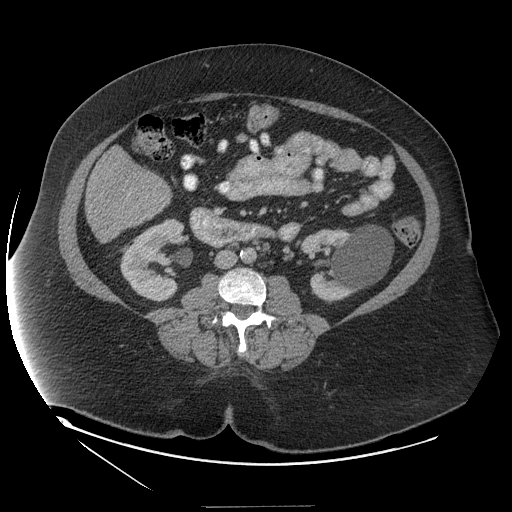
Contrast-enhanced abdominal CT (liver protocol), one axial slice; slice 34 of 127 in the series (ordered by position); reconstruction kernel STANDARD; 140 kVp; soft-tissue window (W 400 / L 40 HU); 2.5 mm slice thickness; 512 × 512 image matrix, field of view 480 × 480 mm. Case-level facts recorded for this patient, not image findings: diagnosis: hepatocellular carcinoma (patient treated with transarterial chemoembolisation; whether this scan precedes or follows treatment is not stated here); TNM stage (as recorded): Stage-II; Child-Pugh class: A; tumour differentiation: well differentiated; tumour nodularity: multinodular.
Structures marked on this image (semi-automatic segmentation, software-assisted and operator-edited):
- liver parenchyma outside the tumour (the mass and vessels are separate outlines, so this box may not span the whole liver): box from (x=84, y=168) to (x=170, y=242) px